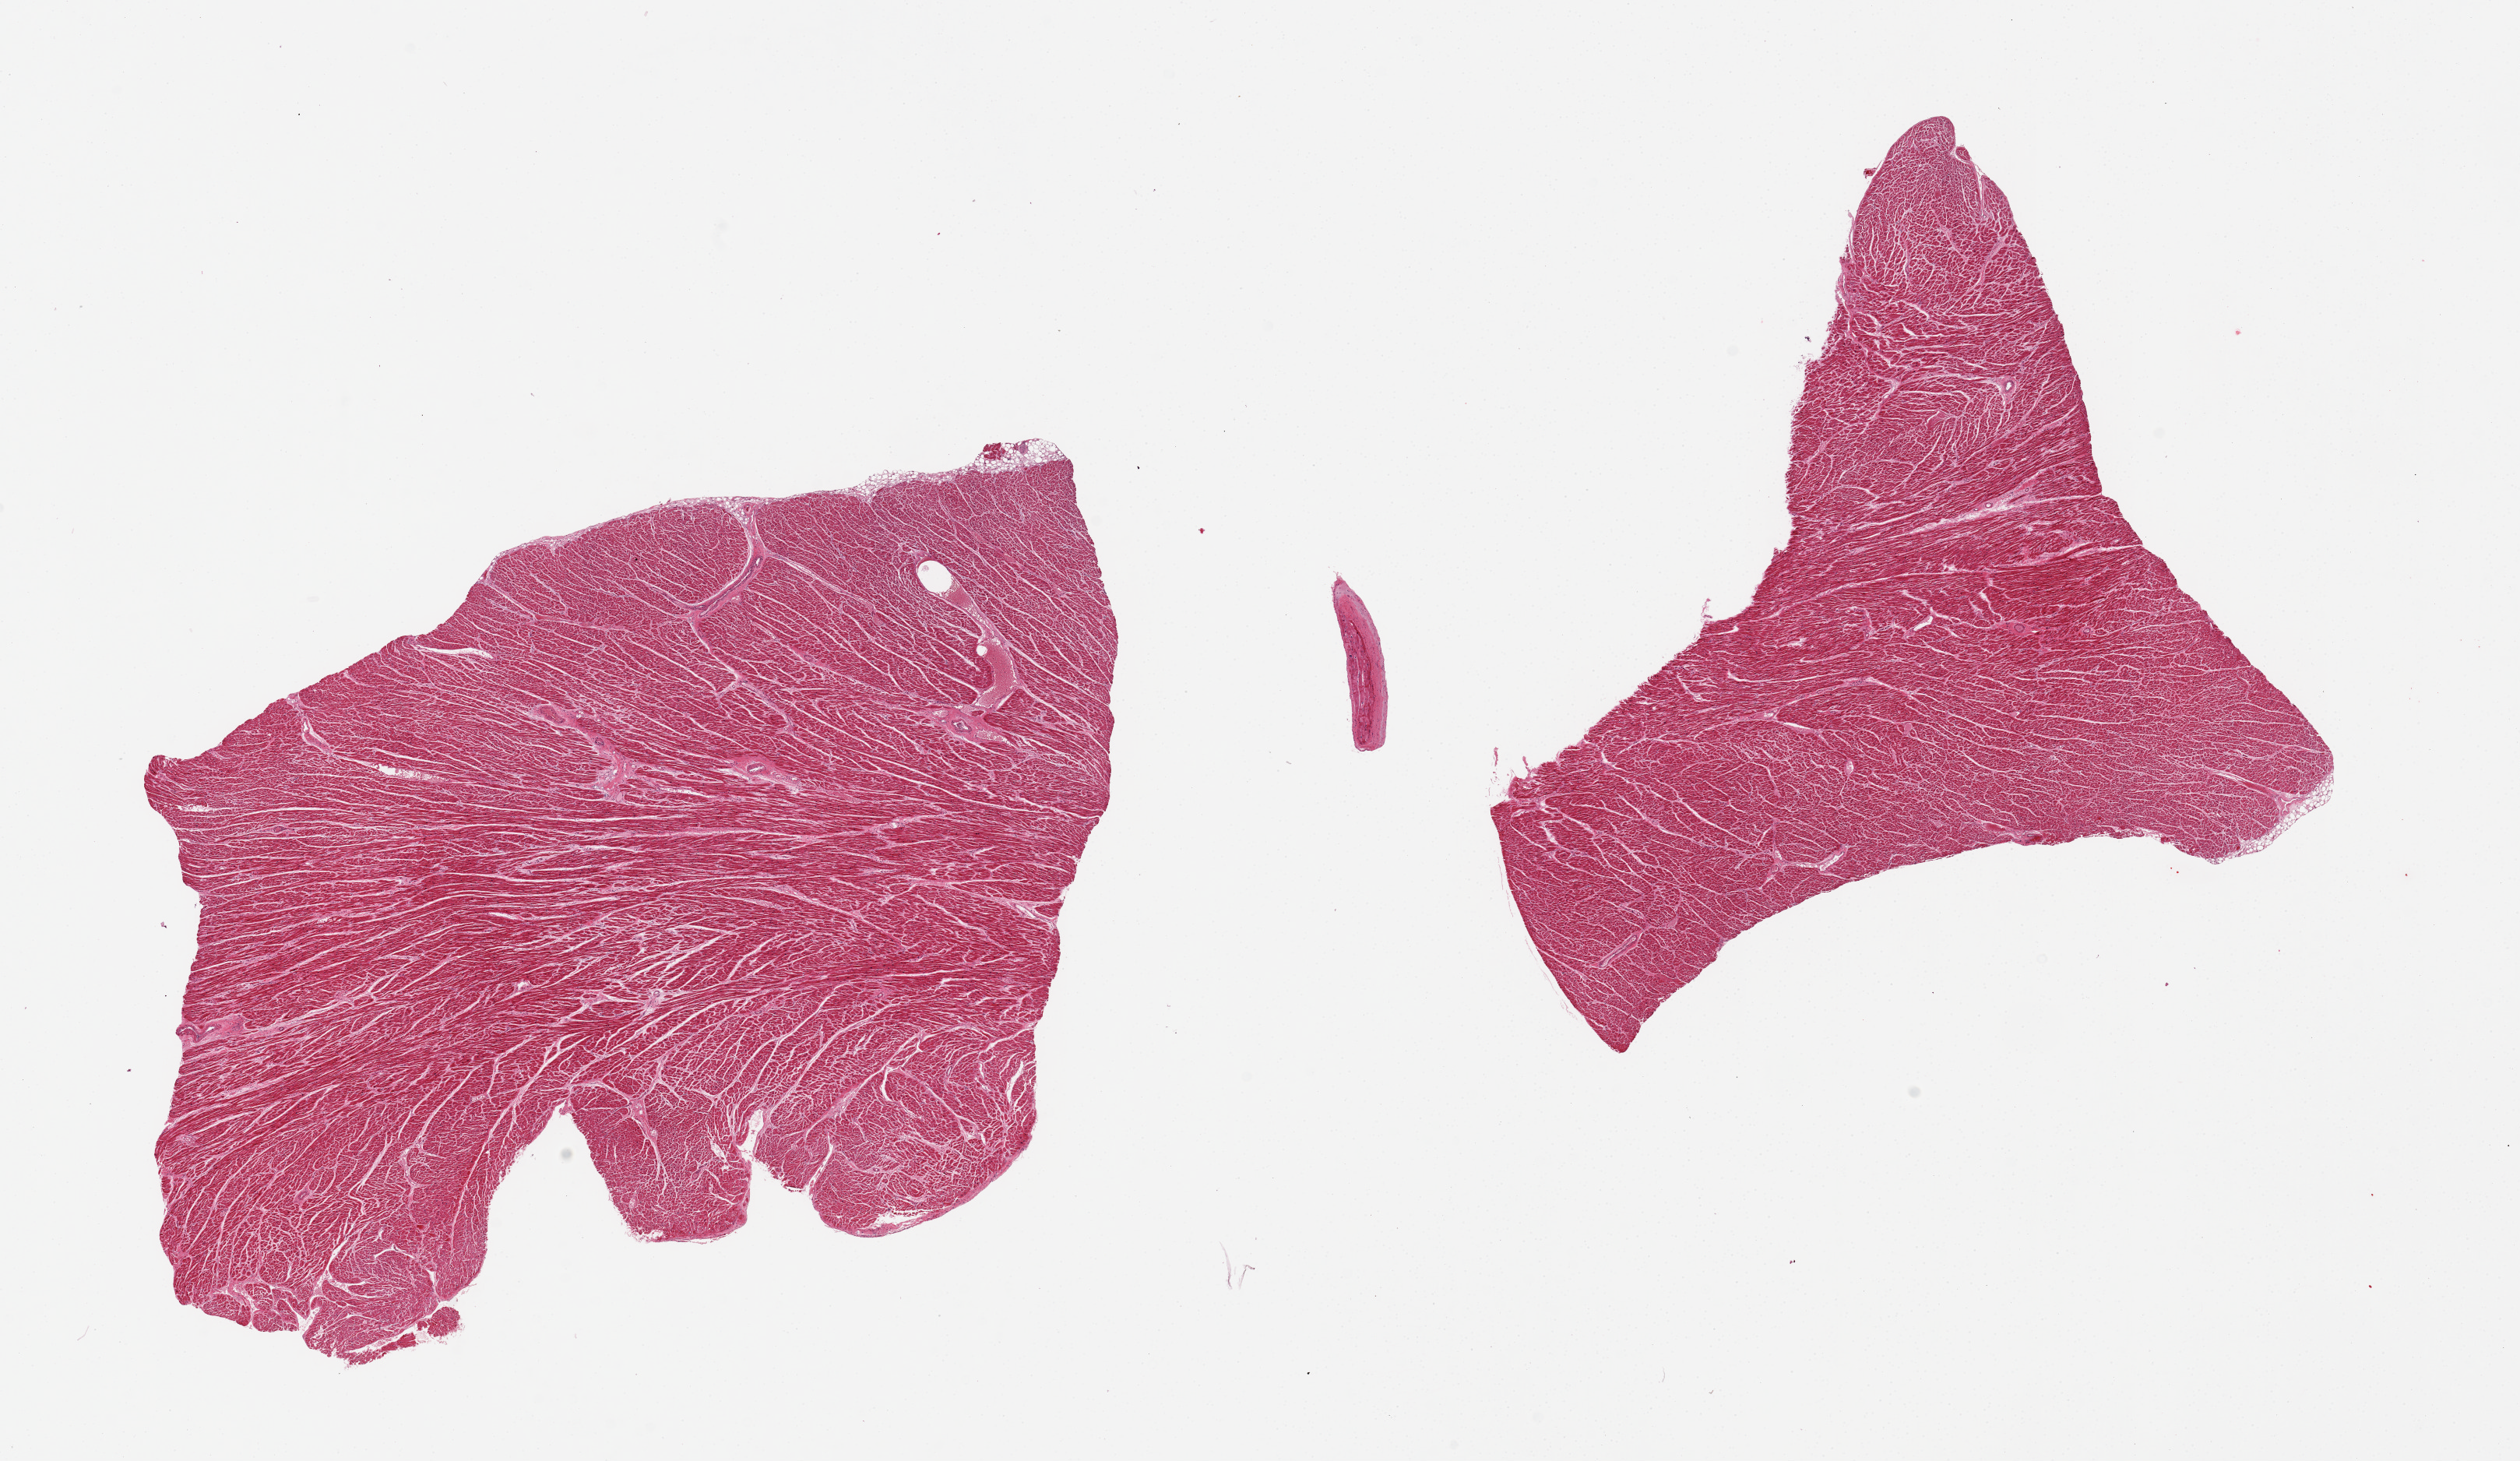
H&E whole-slide image — low-resolution overview of the scanned area, about 25.6 x 14.8 mm. PAXgene-fixed paraffin-embedded (PFPE) section. Sampled site (target tissue): heart. Donor tissue sample. Donor: male.
* reviewer comment on this tissue sample: 2 pieces. Hypertrophied fibers